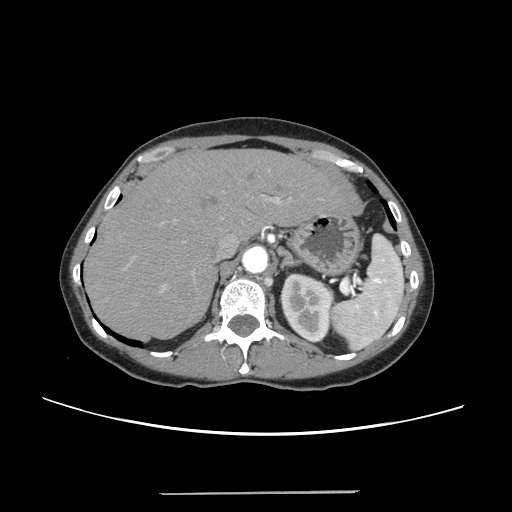
Contrast-enhanced abdominal CT, one axial slice; 120 kVp; intravenous contrast given; soft-tissue window (W 400 / L 40 HU); 1.25 mm slice thickness; 512 × 512 image matrix. Female patient, age 60 years. From the clinical record (not read from this slice): diagnosis: colorectal cancer liver metastases, imaged before liver resection; multiple liver metastases: no.
Outlined on this slice (expert manual segmentation):
- liver: bounding box [x1, y1, x2, y2] px = [86, 150, 349, 339]
- planned liver remnant (the part of the liver to remain after resection): [87, 150, 348, 339]
- portal vein (with intrahepatic branches): [133, 169, 293, 293]